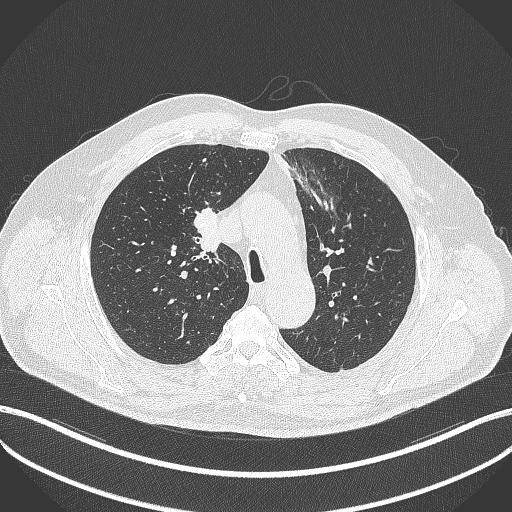
Chest CT, one axial slice. Position 279 of 411 along the scan axis. Reconstruction kernel B70f. Lung window (W 1500 / L -600 HU). 1 mm slice thickness. 512 × 512 image matrix, field of view 400 × 400 mm. Patient: male, 60 years. From the clinical record (not read from this slice): clinical TNM (as recorded): T1b N1 M0.
Structures marked on this image (rectangle marked by the reading radiologist):
- lung tumour (recorded histology: squamous cell carcinoma): bounding box (x1, y1, x2, y2) in pixels: (194, 204, 223, 255)